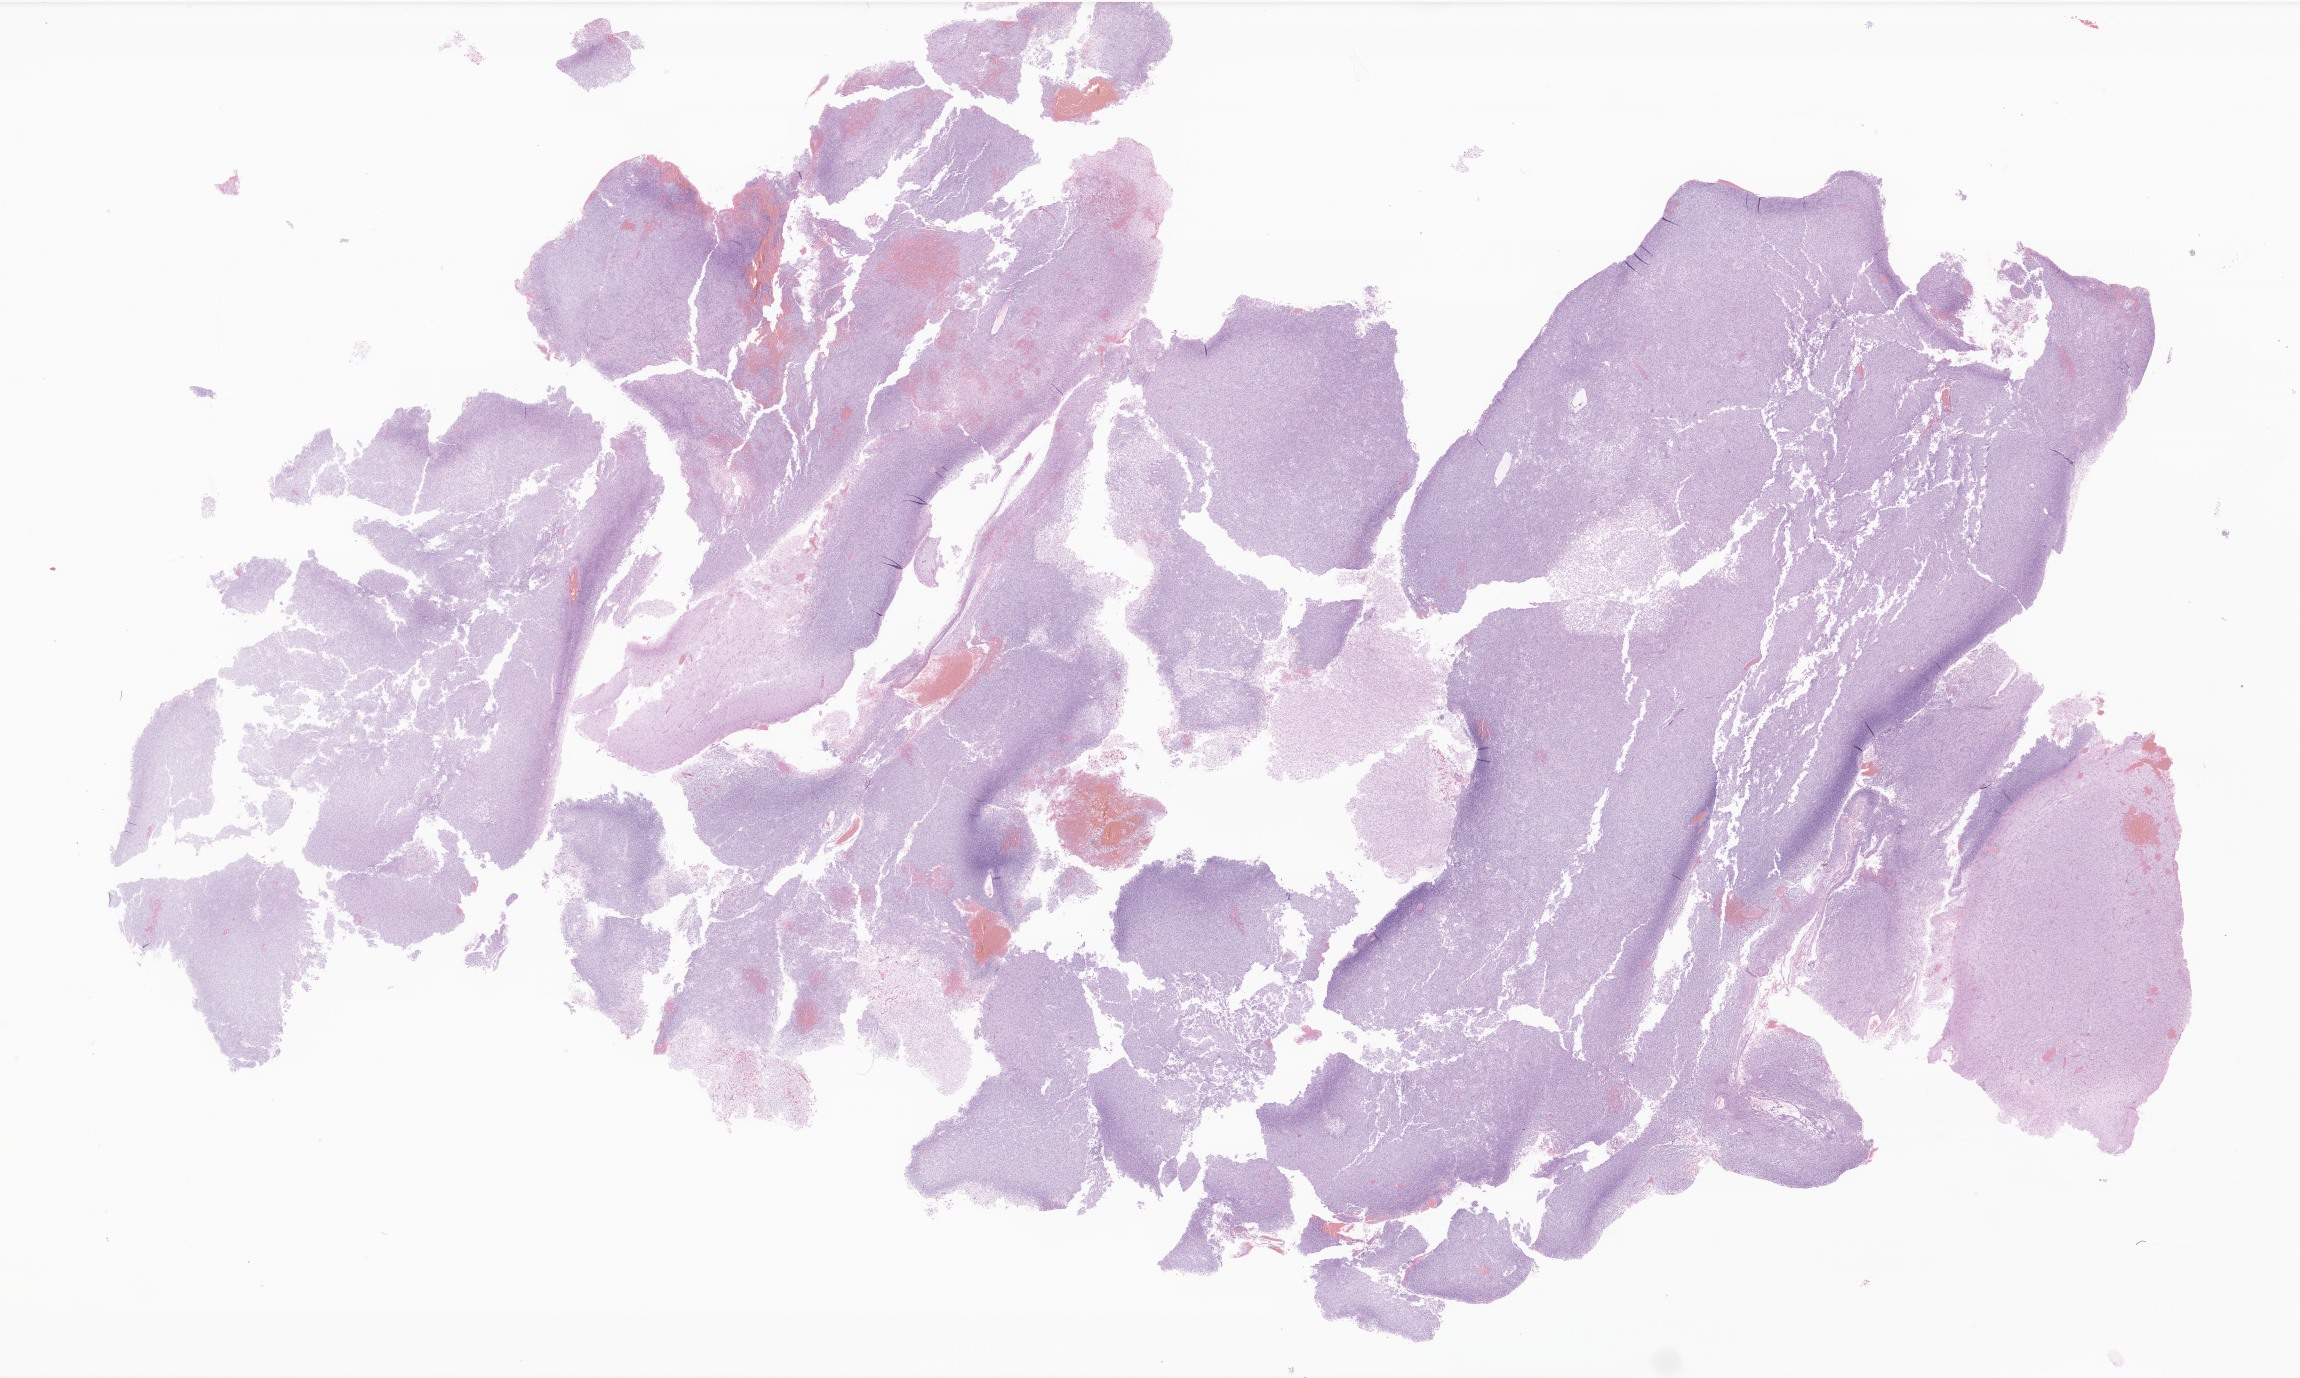
Digitized hematoxylin and eosin (H&E)-stained section of tumor tissue from the temporal lobe — whole scanned area (about 38.8 x 23.2 mm) shown as a low-resolution overview; FFPE section. Male patient, age 215 days.
Recorded diagnosis: Neoplasm, malignant.